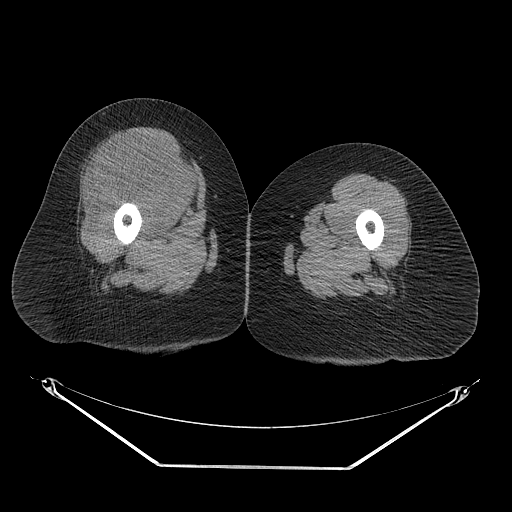
CT of an extremity soft-tissue mass (from a PET/CT study), one axial slice; position 32 of 267 along the scan axis; reconstruction kernel STANDARD; 140 kVp; soft-tissue window (W 400 / L 40 HU); 3.75 mm slice thickness; 512 × 512 image matrix, field of view 500 × 500 mm. Female patient. From the clinical record (not read from this slice): histological type: malignant solitary fibrous tumor; grade: intermediate; site of the primary tumour: right thigh.
Annotated regions visible in this slice (expert contour drawn on MRI and transferred to this co-registered scan by the dataset authors):
- gross tumour volume including surrounding oedema: bounding box (x1, y1, x2, y2) in pixels: (93, 132, 206, 222)
- gross tumour volume (mass): (98, 132, 202, 218)